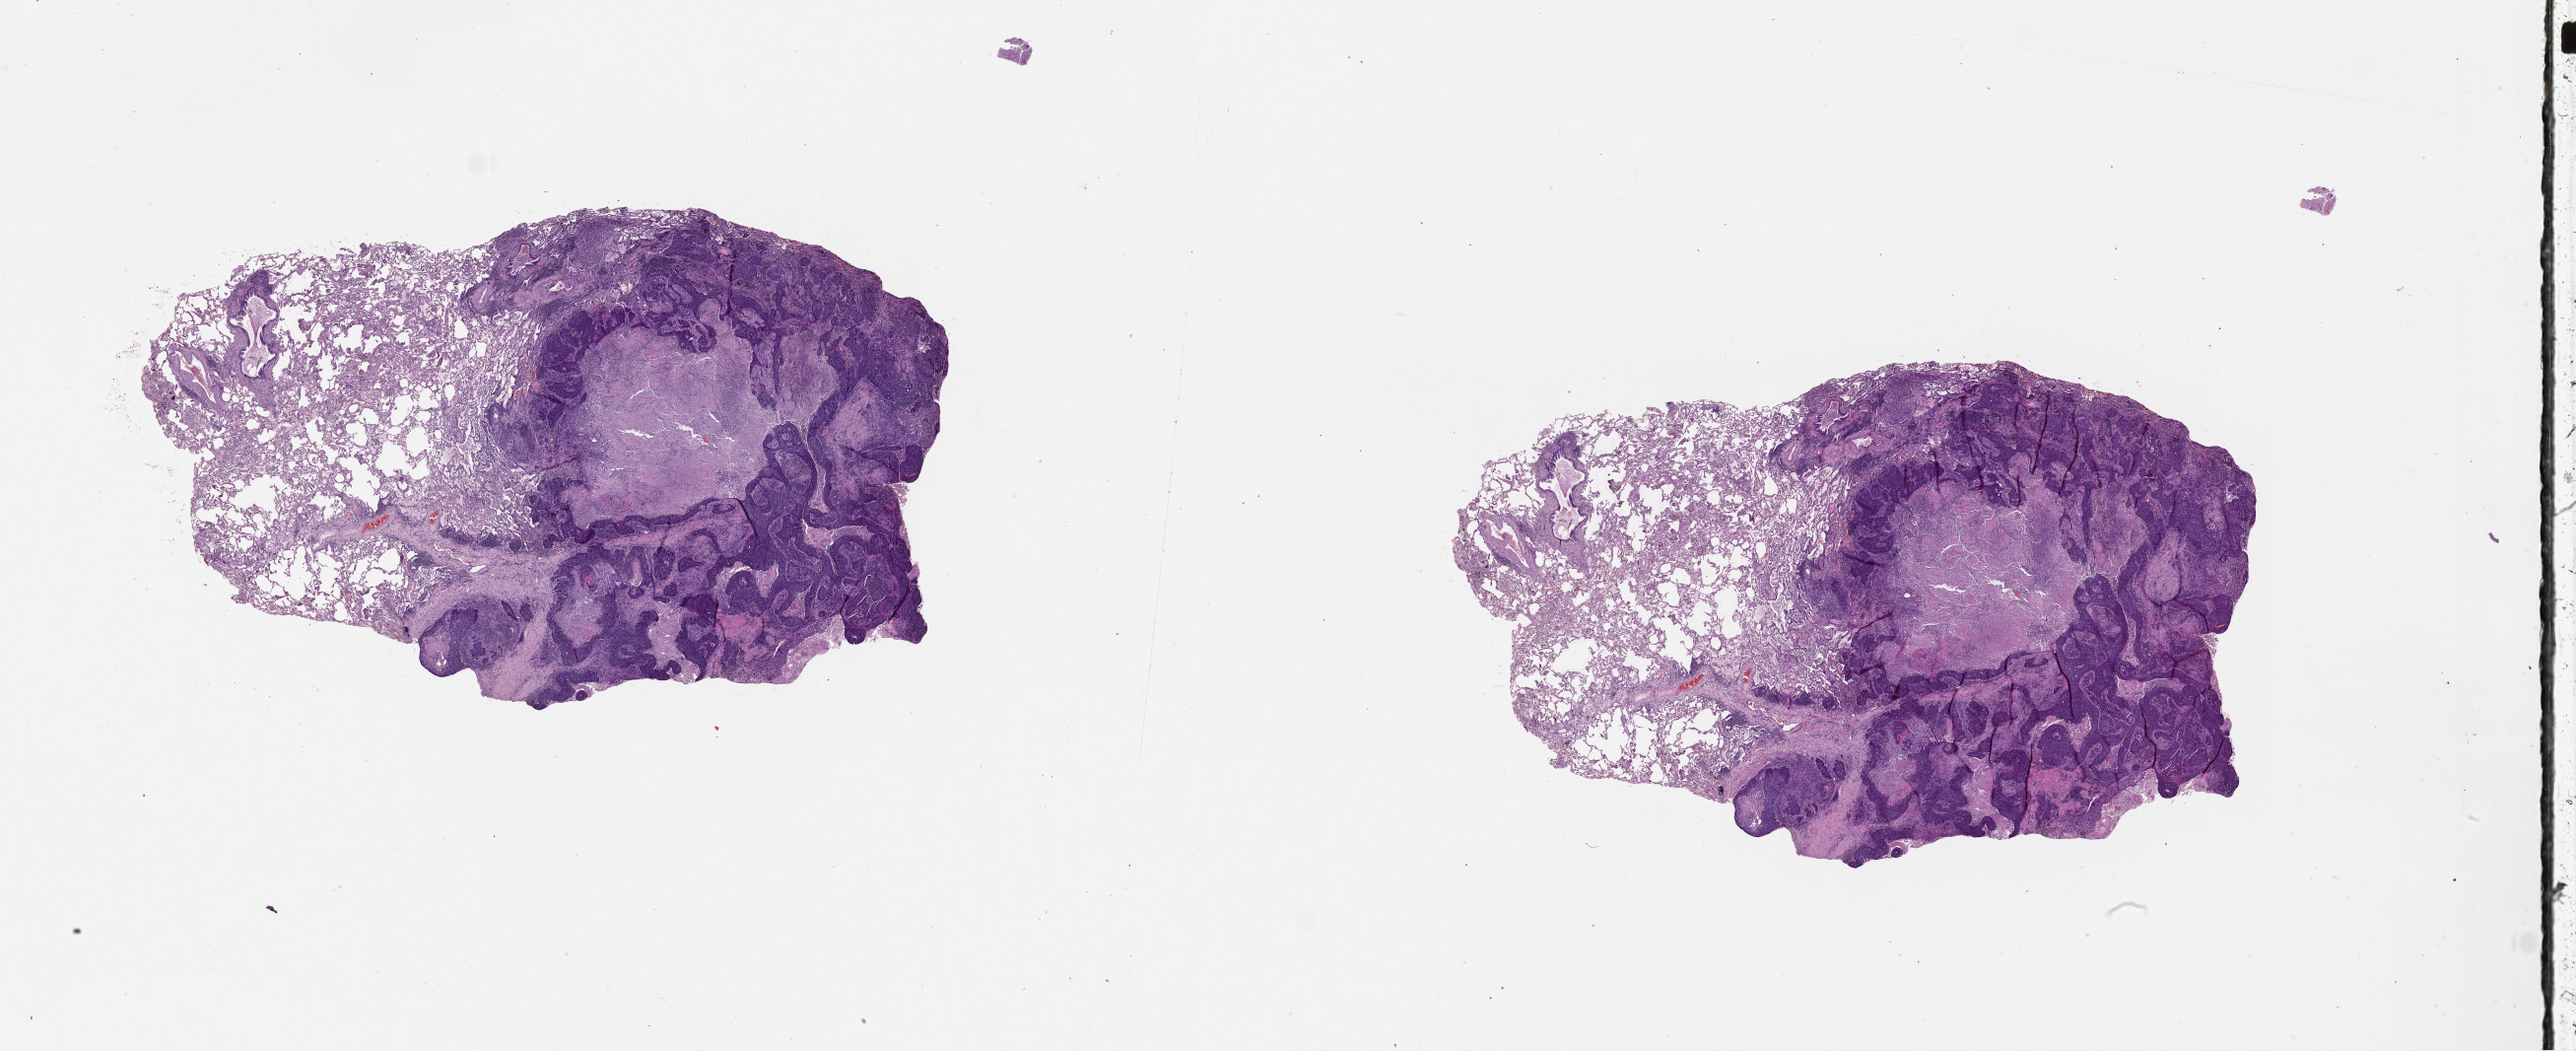
Digitized H&E tissue section (whole slide), a low-resolution overview of the entire scanned area, about 42.1 x 17.2 mm; tumour tissue sample, lung. 62-year-old female patient.
Patient diagnosis (cohort enrolment): squamous cell carcinoma (lung).